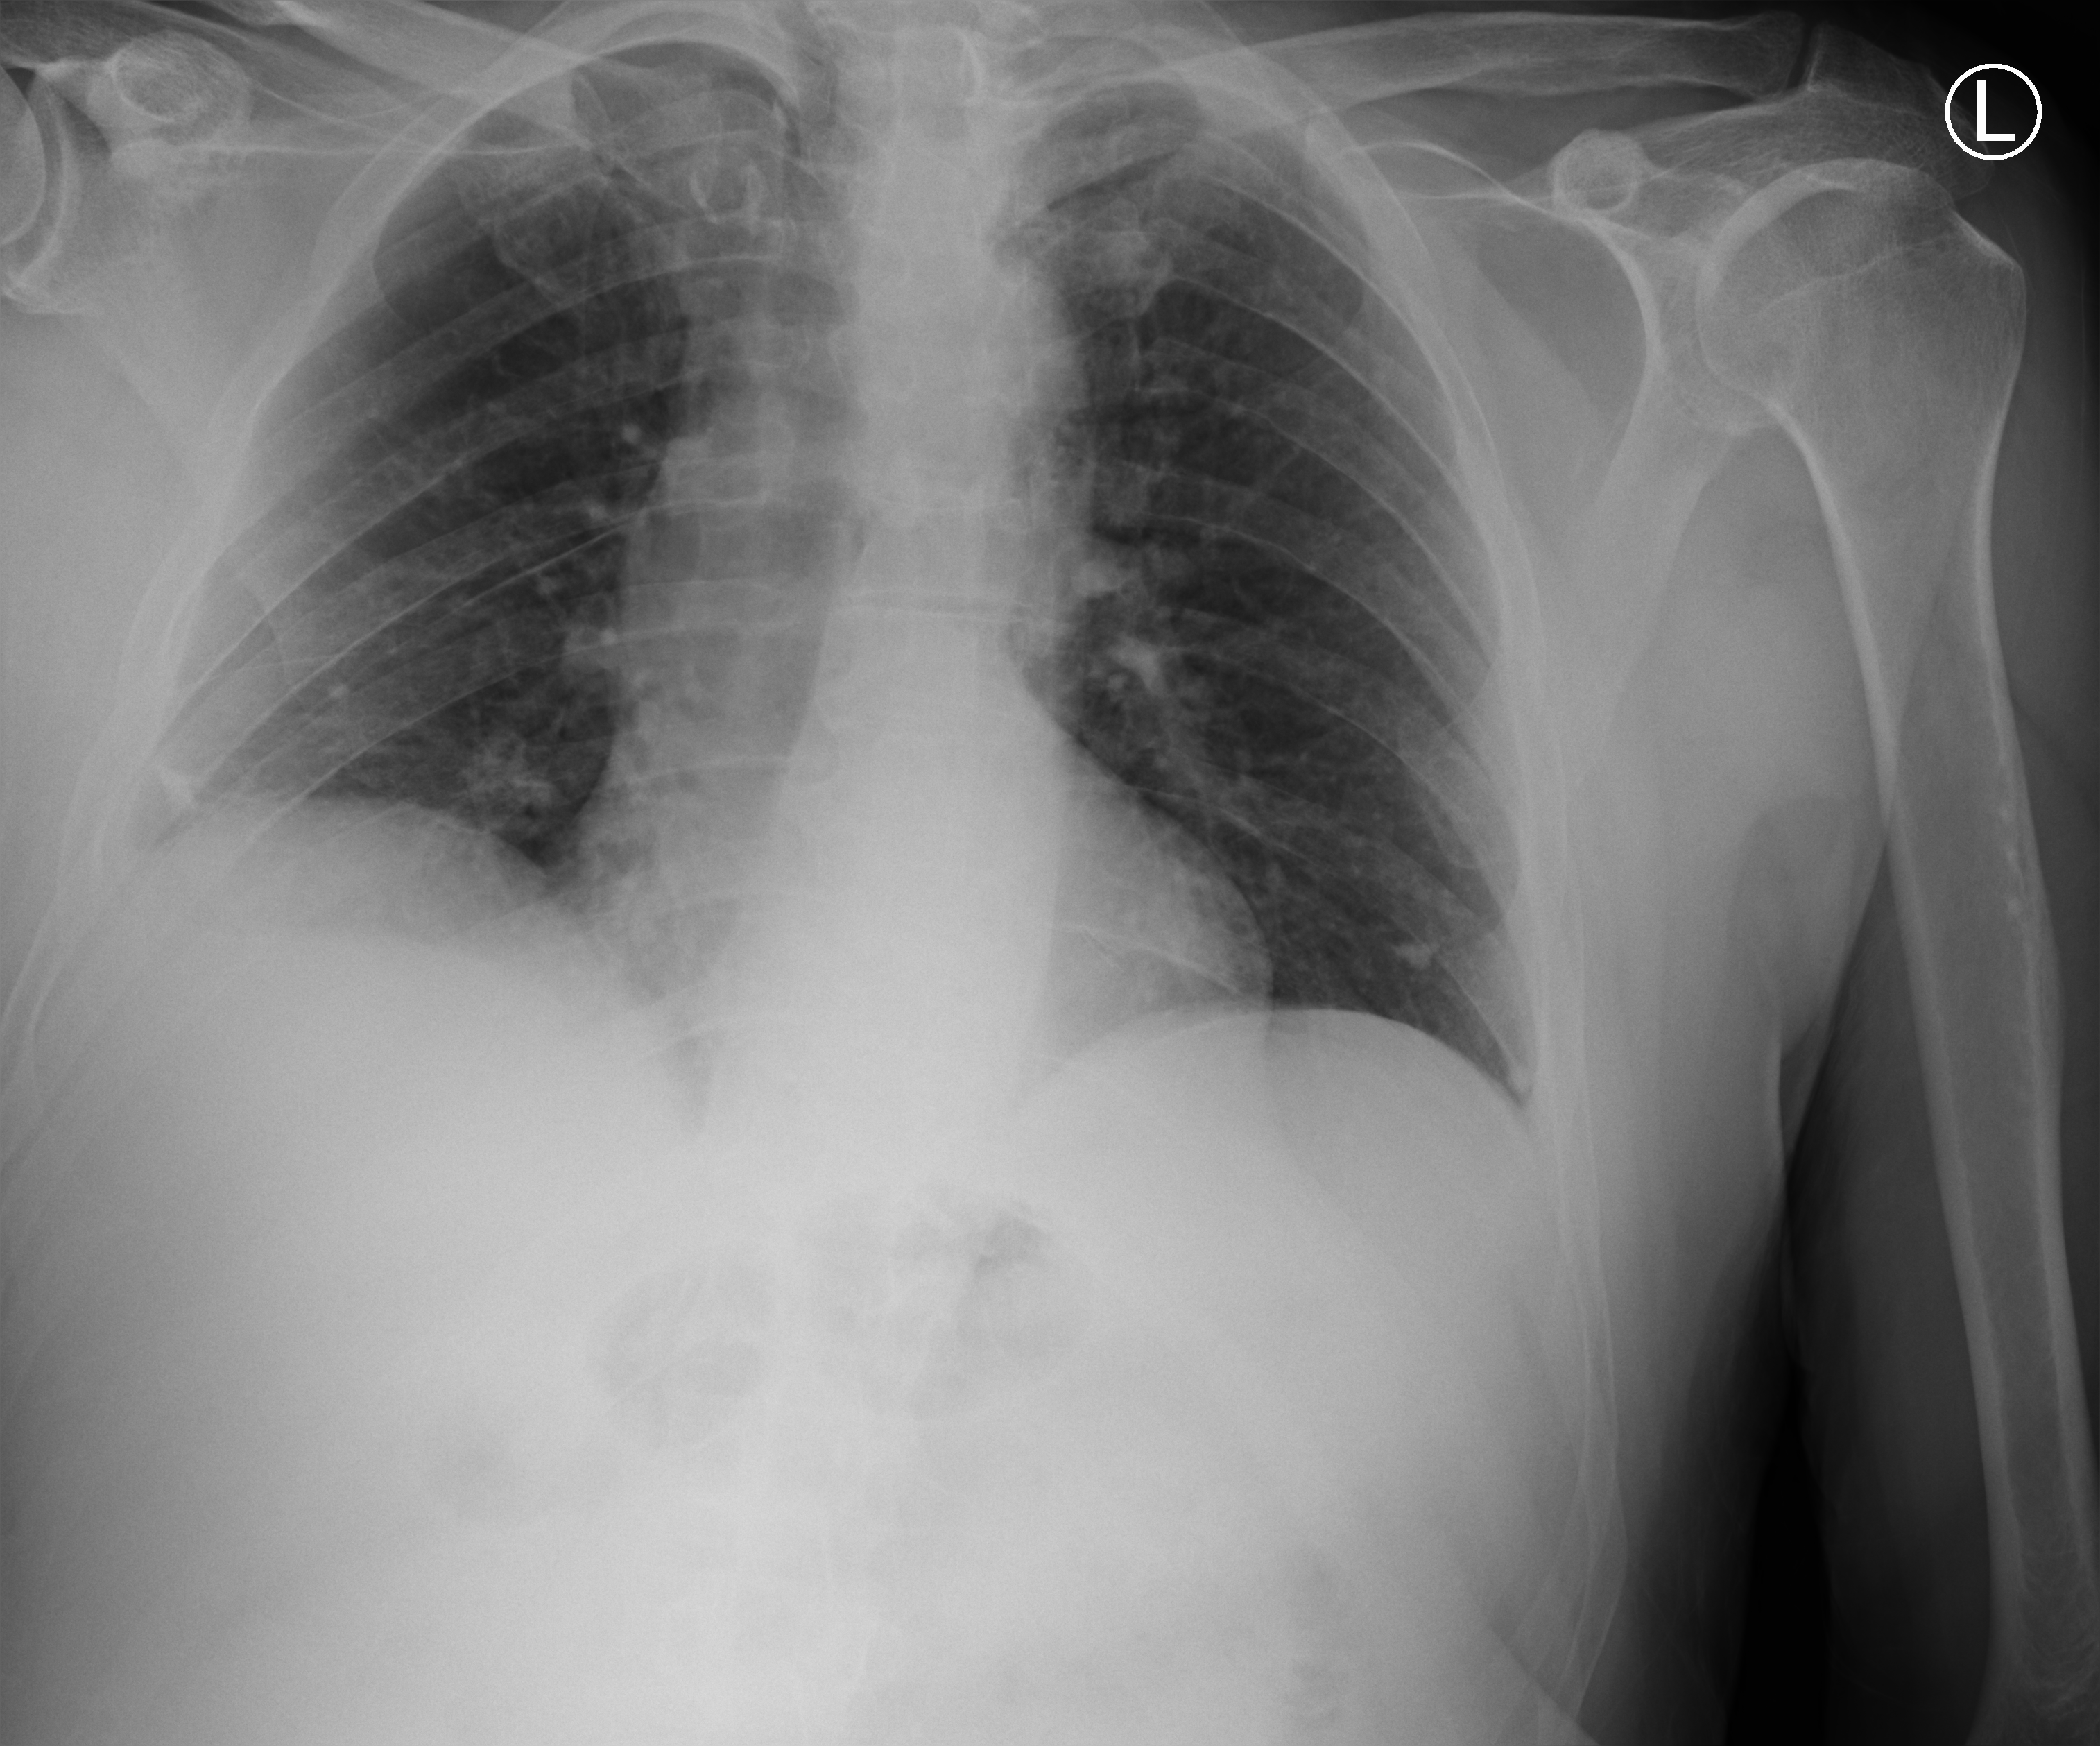
Portable chest radiograph. Male patient hospitalised with COVID-19, age 75–90 years.
Hospital-stay facts (about this admission, not read from this image; timing relative to this image not recorded): length of hospital stay: 7 days; hypertension (admission record): no.